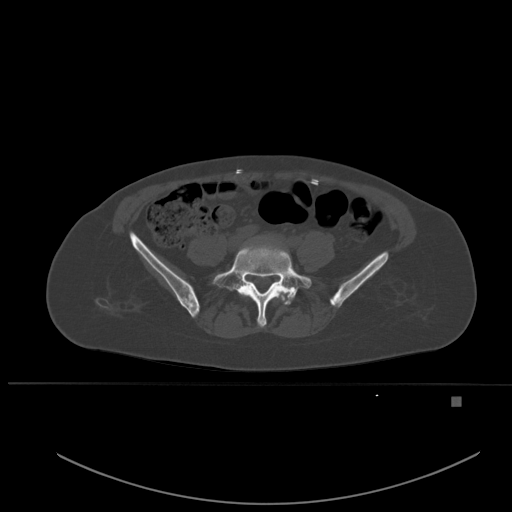
CT including the spine, one axial slice; slice 157 of 651 in the series (ordered by position); bone window (W 1800 / L 400 HU); 512 × 512 image matrix, field of view 443 × 443 mm. Female patient, age 49 years. From the clinical record (not read from this slice): primary cancer: breast.
Structures marked on this image (semi-automatic segmentation, software-assisted and operator-edited):
- L4 vertebra: bounding box [x1, y1, x2, y2] px = [242, 290, 285, 300]
- L5 vertebra: [213, 246, 312, 327]